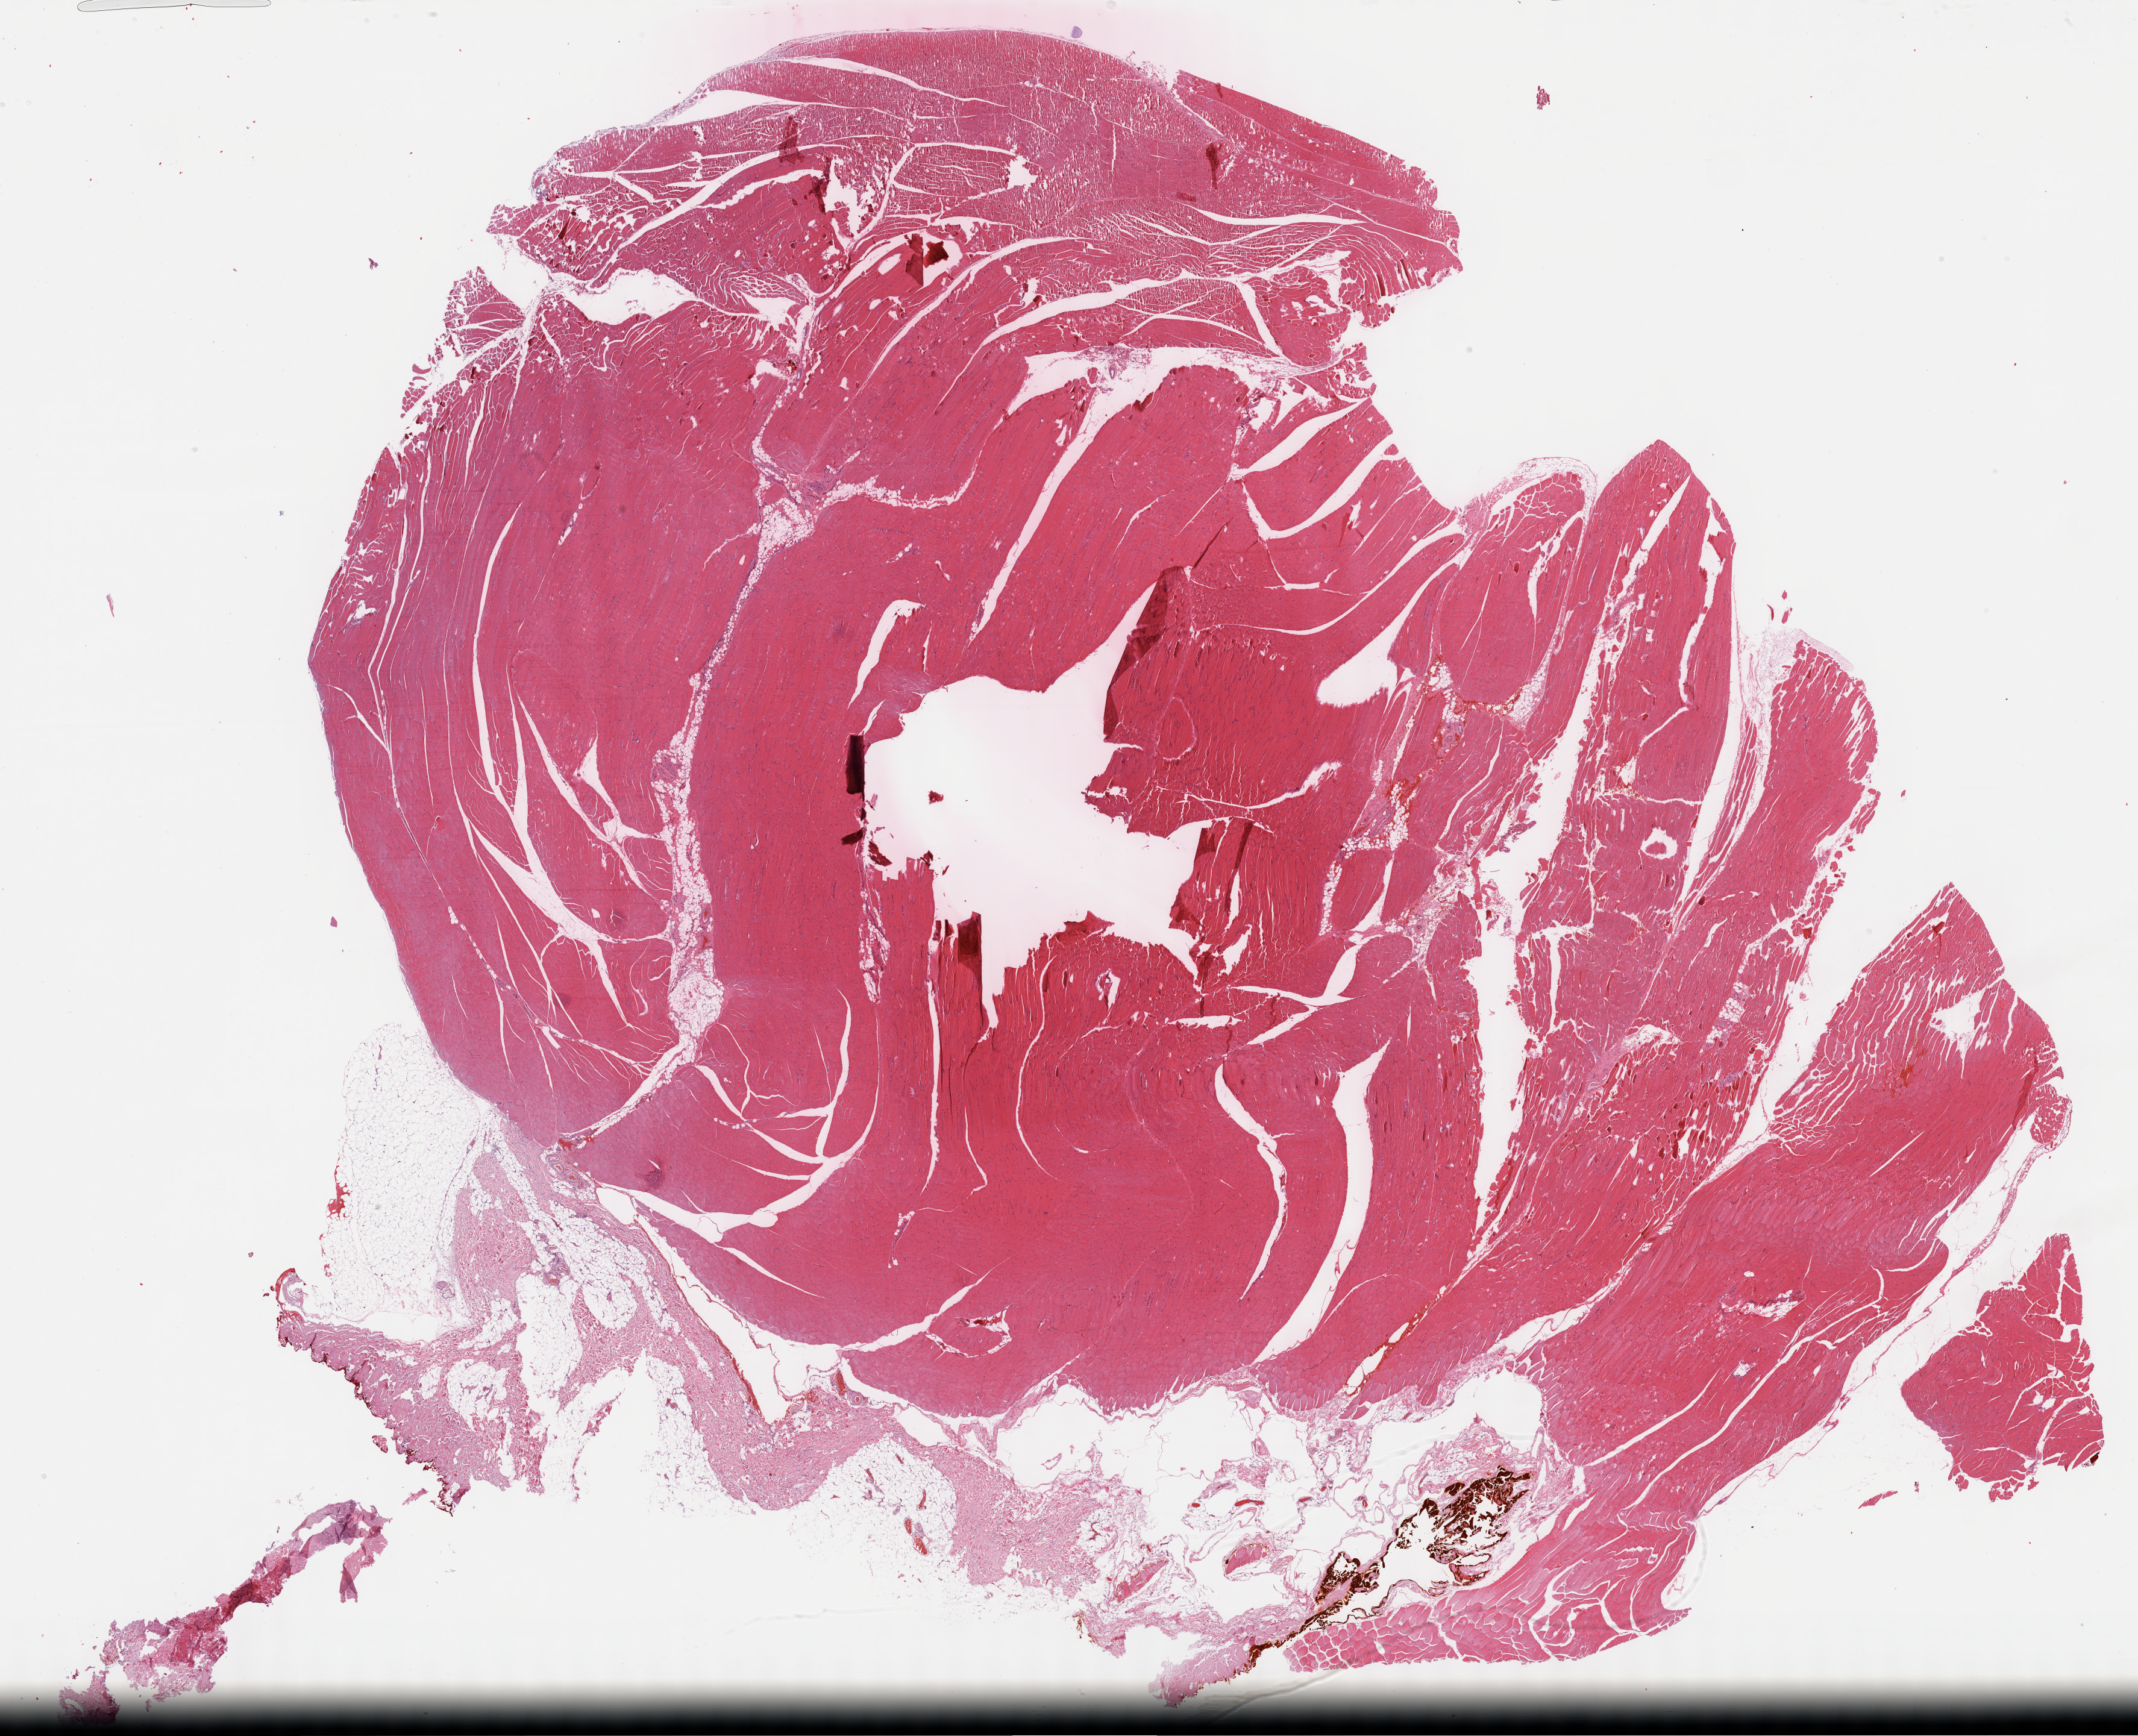
H&E whole-slide image — shown as a low-resolution overview of the whole scanned area (about 28.7 x 23.3 mm); formalin-fixed paraffin-embedded (FFPE) diagnostic section; primary tumour sample from the connective, subcutaneous and other soft tissues. Male patient; age at initial diagnosis 35 years.
Pathologic diagnosis: Fibromyxosarcoma (connective, subcutaneous and other soft tissues of lower limb and hip).